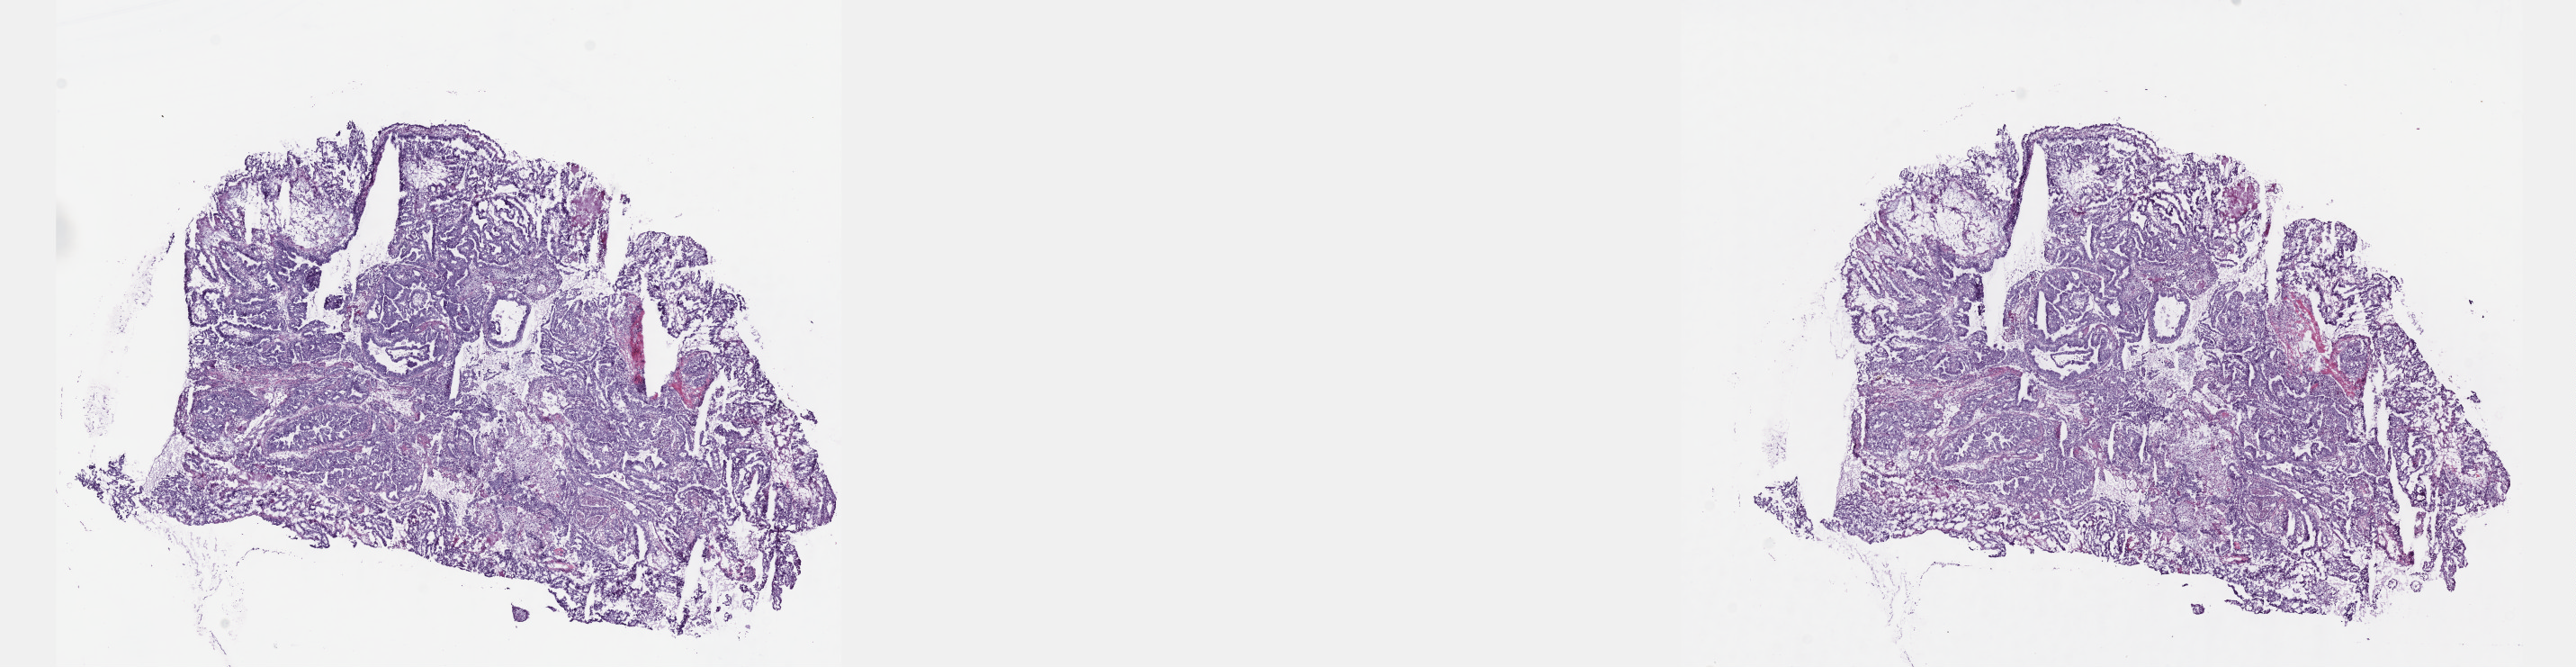
Whole-slide histology image, Hematoxylin and eosin (H&E) stained, a low-resolution overview of the entire scanned area, about 23.1 x 6.0 mm (from a 40x scan). Frozen section from the top of the tissue portion. Primary tumour sample from the cervix. Patient: female, age at initial diagnosis 58 years. Histologic grade: G3 (poorly differentiated). Pathologist review of this section (percent, as recorded): tumour cells 100%, tumour nuclei 65%, normal cells 0%, stromal cells 0%, necrosis 0%. Infiltration values recorded for this section: lymphocyte infiltration 8%, monocyte infiltration 1%, neutrophil infiltration 2%.
• FIGO stage: IB
• pathologic diagnosis: Mucinous adenocarcinoma, endocervical type (cervix uteri)